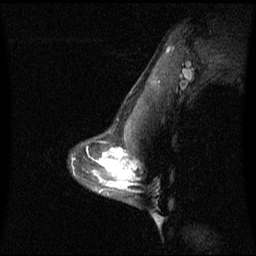
Breast MRI (dynamic contrast-enhanced), one sagittal slice. Slice 47 of 60 in the series (ordered by position). Dynamic contrast-enhanced series, image 2 of 3 at this slice position (ordered by acquisition). 1.5 T. TE 4.2 ms, TR 8.4 ms. 256 × 256 image matrix, field of view 240 × 240 mm. Patient: female, 42 years. Case-level facts recorded for this patient, not image findings: setting: breast cancer imaged before/during neoadjuvant chemotherapy; receptor status: triple-negative.
Outlined on this slice (semi-automatically segmented with operator editing):
- analysis volume of interest (the breast-tissue region the enhancement analysis was run in; not a lesion): bounding box <106,156,133,197> (left, top, right, bottom; pixels)
- tumour enhancement mask (voxels above the 70 % enhancement threshold inside the analysis volume of interest): <118,166,132,189>